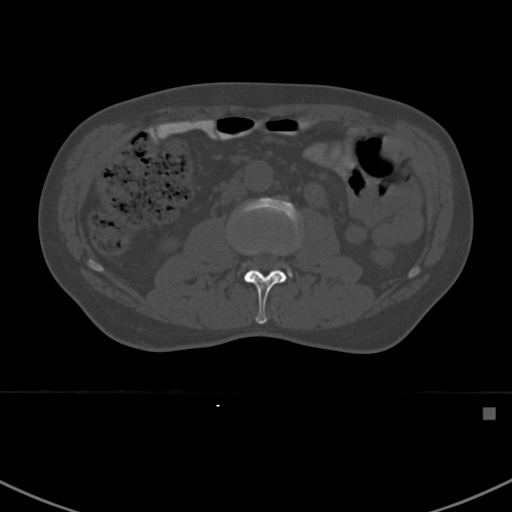
CT including the spine, one axial slice. Position 278 of 412 along the scan axis. Reconstruction kernel Br40s. 120 kVp. Bone window (W 1800 / L 400 HU). 1.5 mm slice thickness. 512 × 512 image matrix. Patient: male, 59 years. From the clinical record (not read from this slice): primary cancer: prostate.
Structures marked on this image (semi-automatically segmented with operator editing):
- L2 vertebra: bounding box (x1, y1, x2, y2) in pixels: (237, 246, 287, 324)
- L3 vertebra: (233, 197, 301, 277)